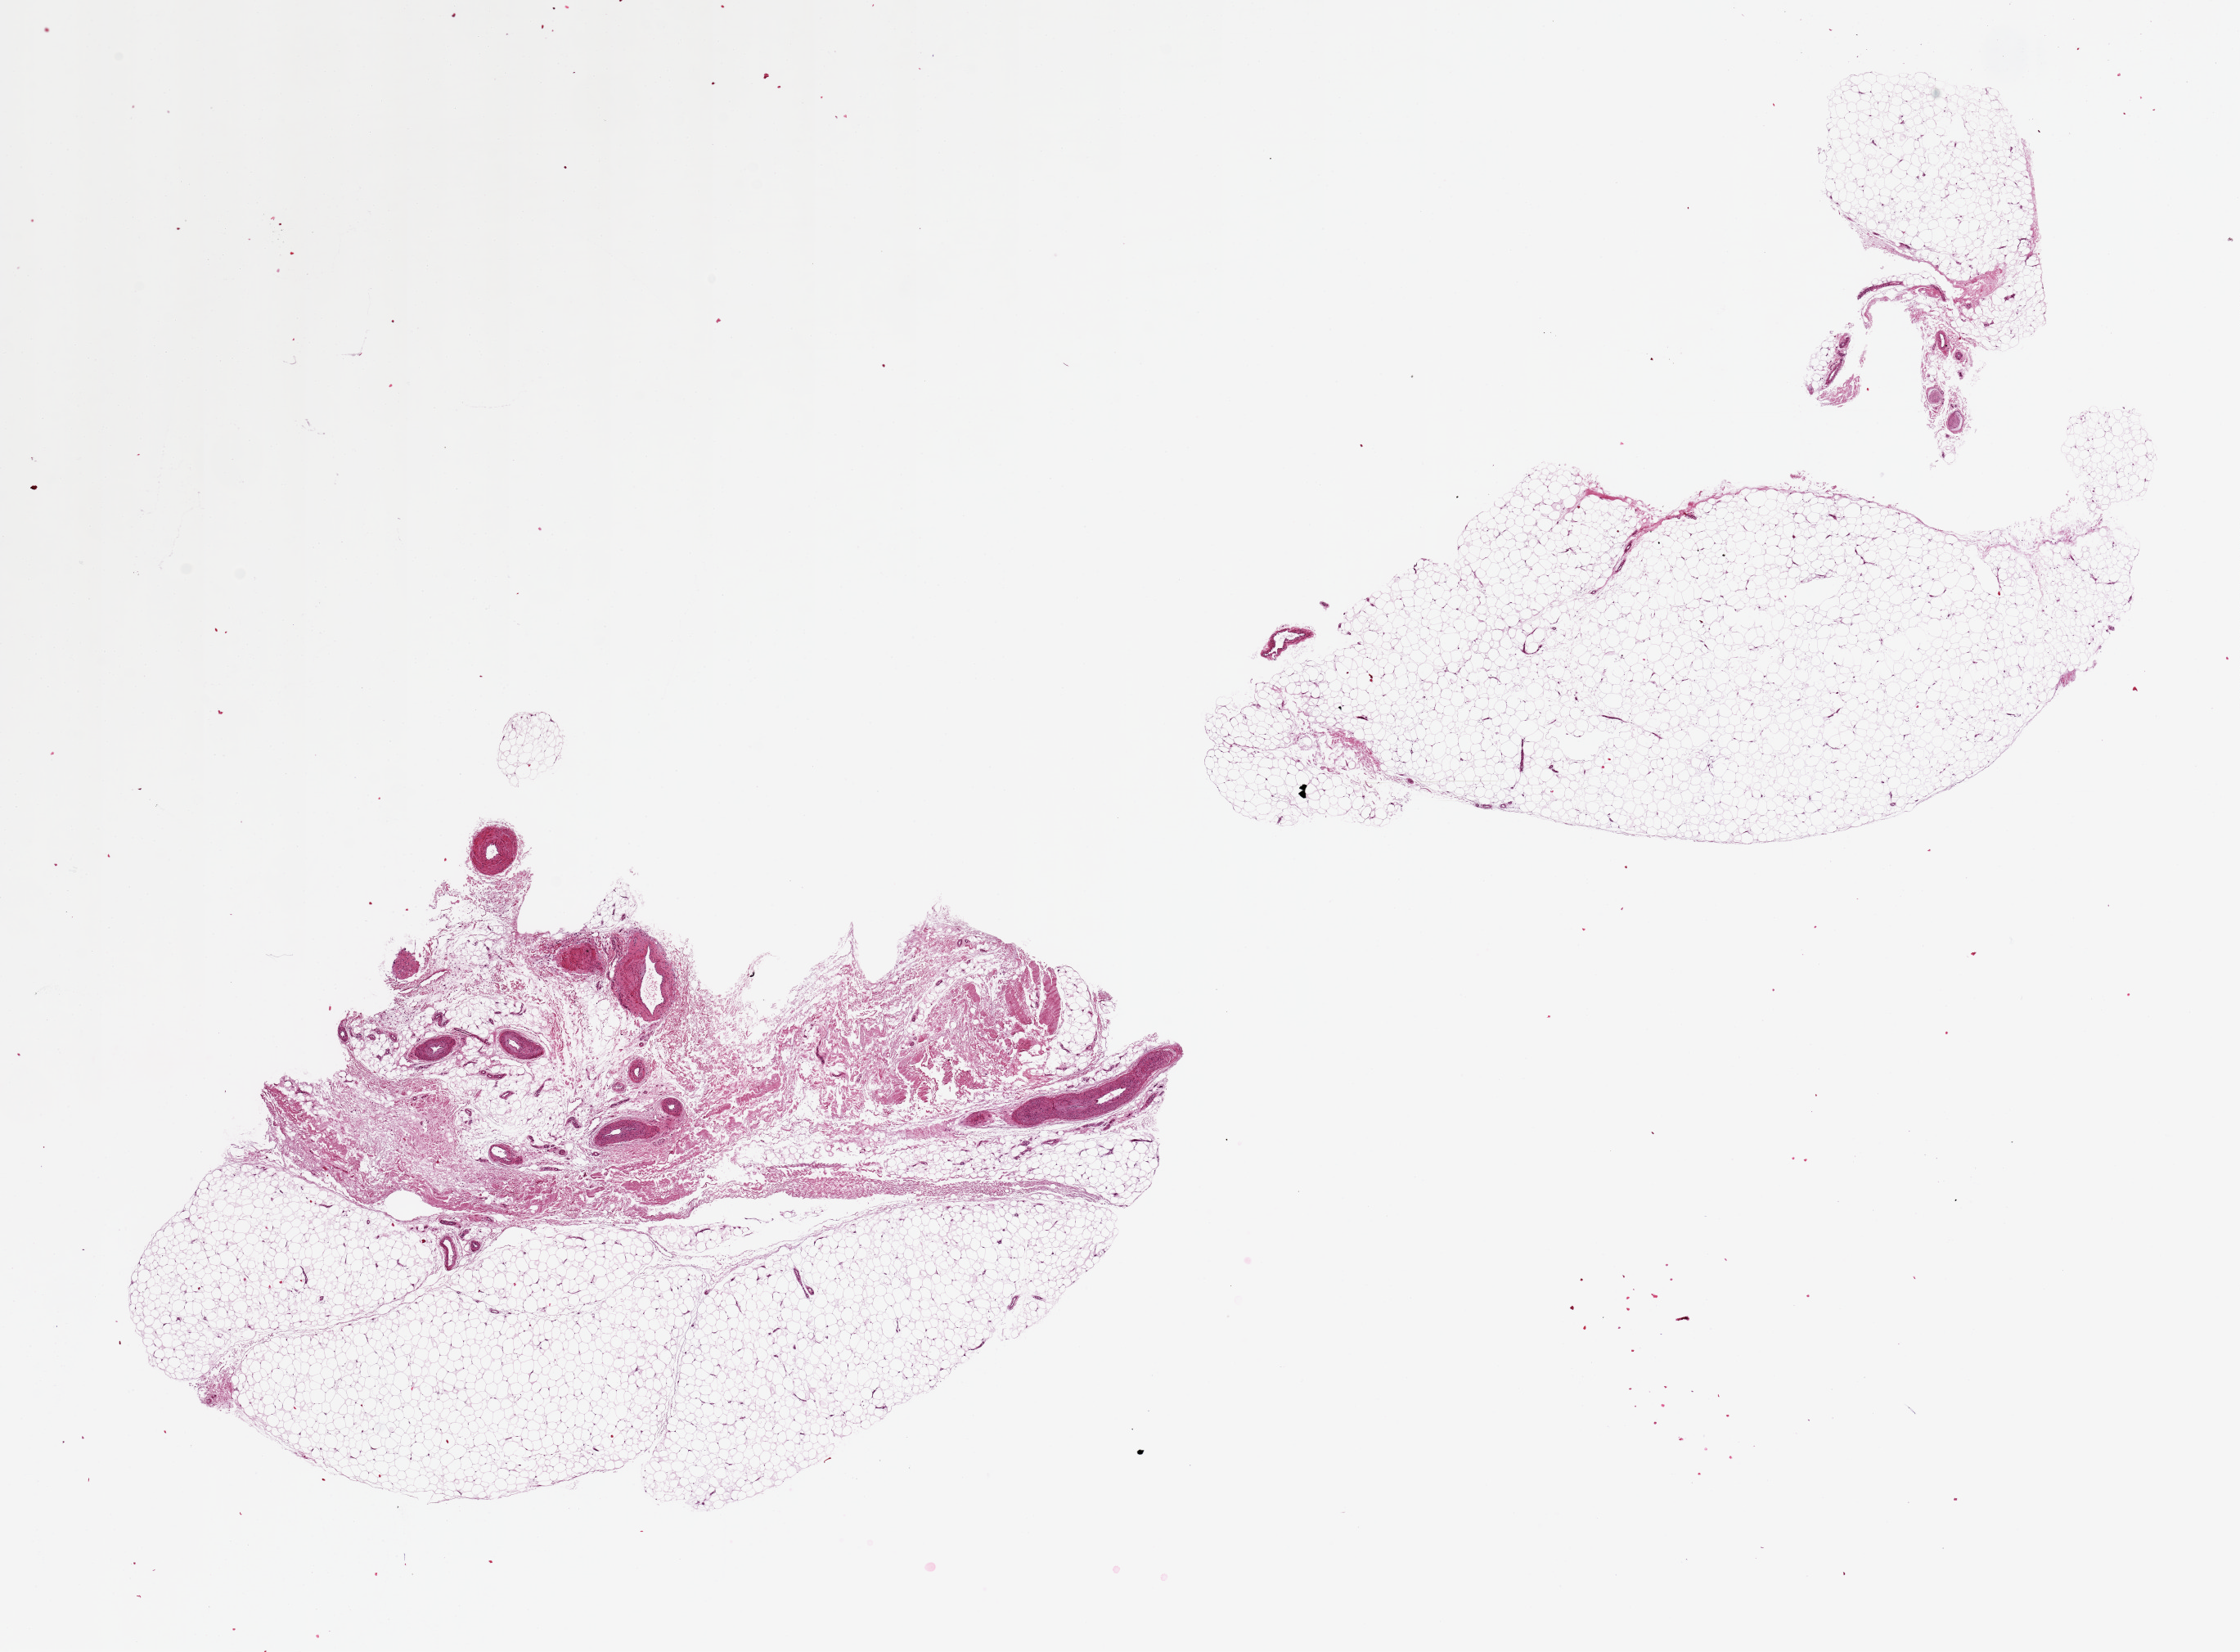
Digitized haematoxylin and eosin-stained section, a low-resolution overview of the entire scanned area, about 21.7 x 16.0 mm. PAXgene-fixed, paraffin-embedded tissue. Target tissue: adipose tissue. Tissue donor sample. Donor sex: male.
- pathologist's review note for this sample: 2 pieces, 10x8 & 10x7mm; 1 is all adipose, other contains 40% fibrovascular tissue